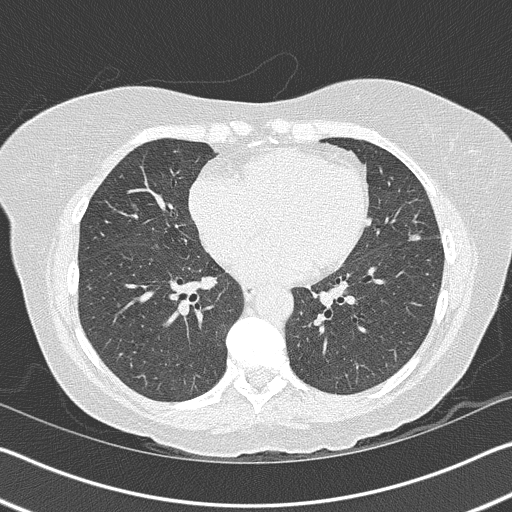
Low-dose screening chest CT, axial slice. First (baseline) screen. Lung window (W 1500 / L -600 HU). 2 mm slice thickness. 120 kVp. Slice 69 of 157 in the series. Female participant, aged 63 years at enrolment. Current smoker at enrolment.
- Lesion marked by an expert reader, bounding box [x1, y1, x2, y2] px = [384, 216, 437, 256].
- The screening reader recorded 3 non-calcified nodules or masses ≥4 mm on this exam (right upper lobe, left upper lobe, lingula); which of them this box marks is not recorded.
- Later outcome: lung cancer diagnosed 1029 days after this screen — bronchiolo-alveolar adenocarcinoma, NOS, lingula, stage IA (AJCC 6th edition), 14 mm at pathology.